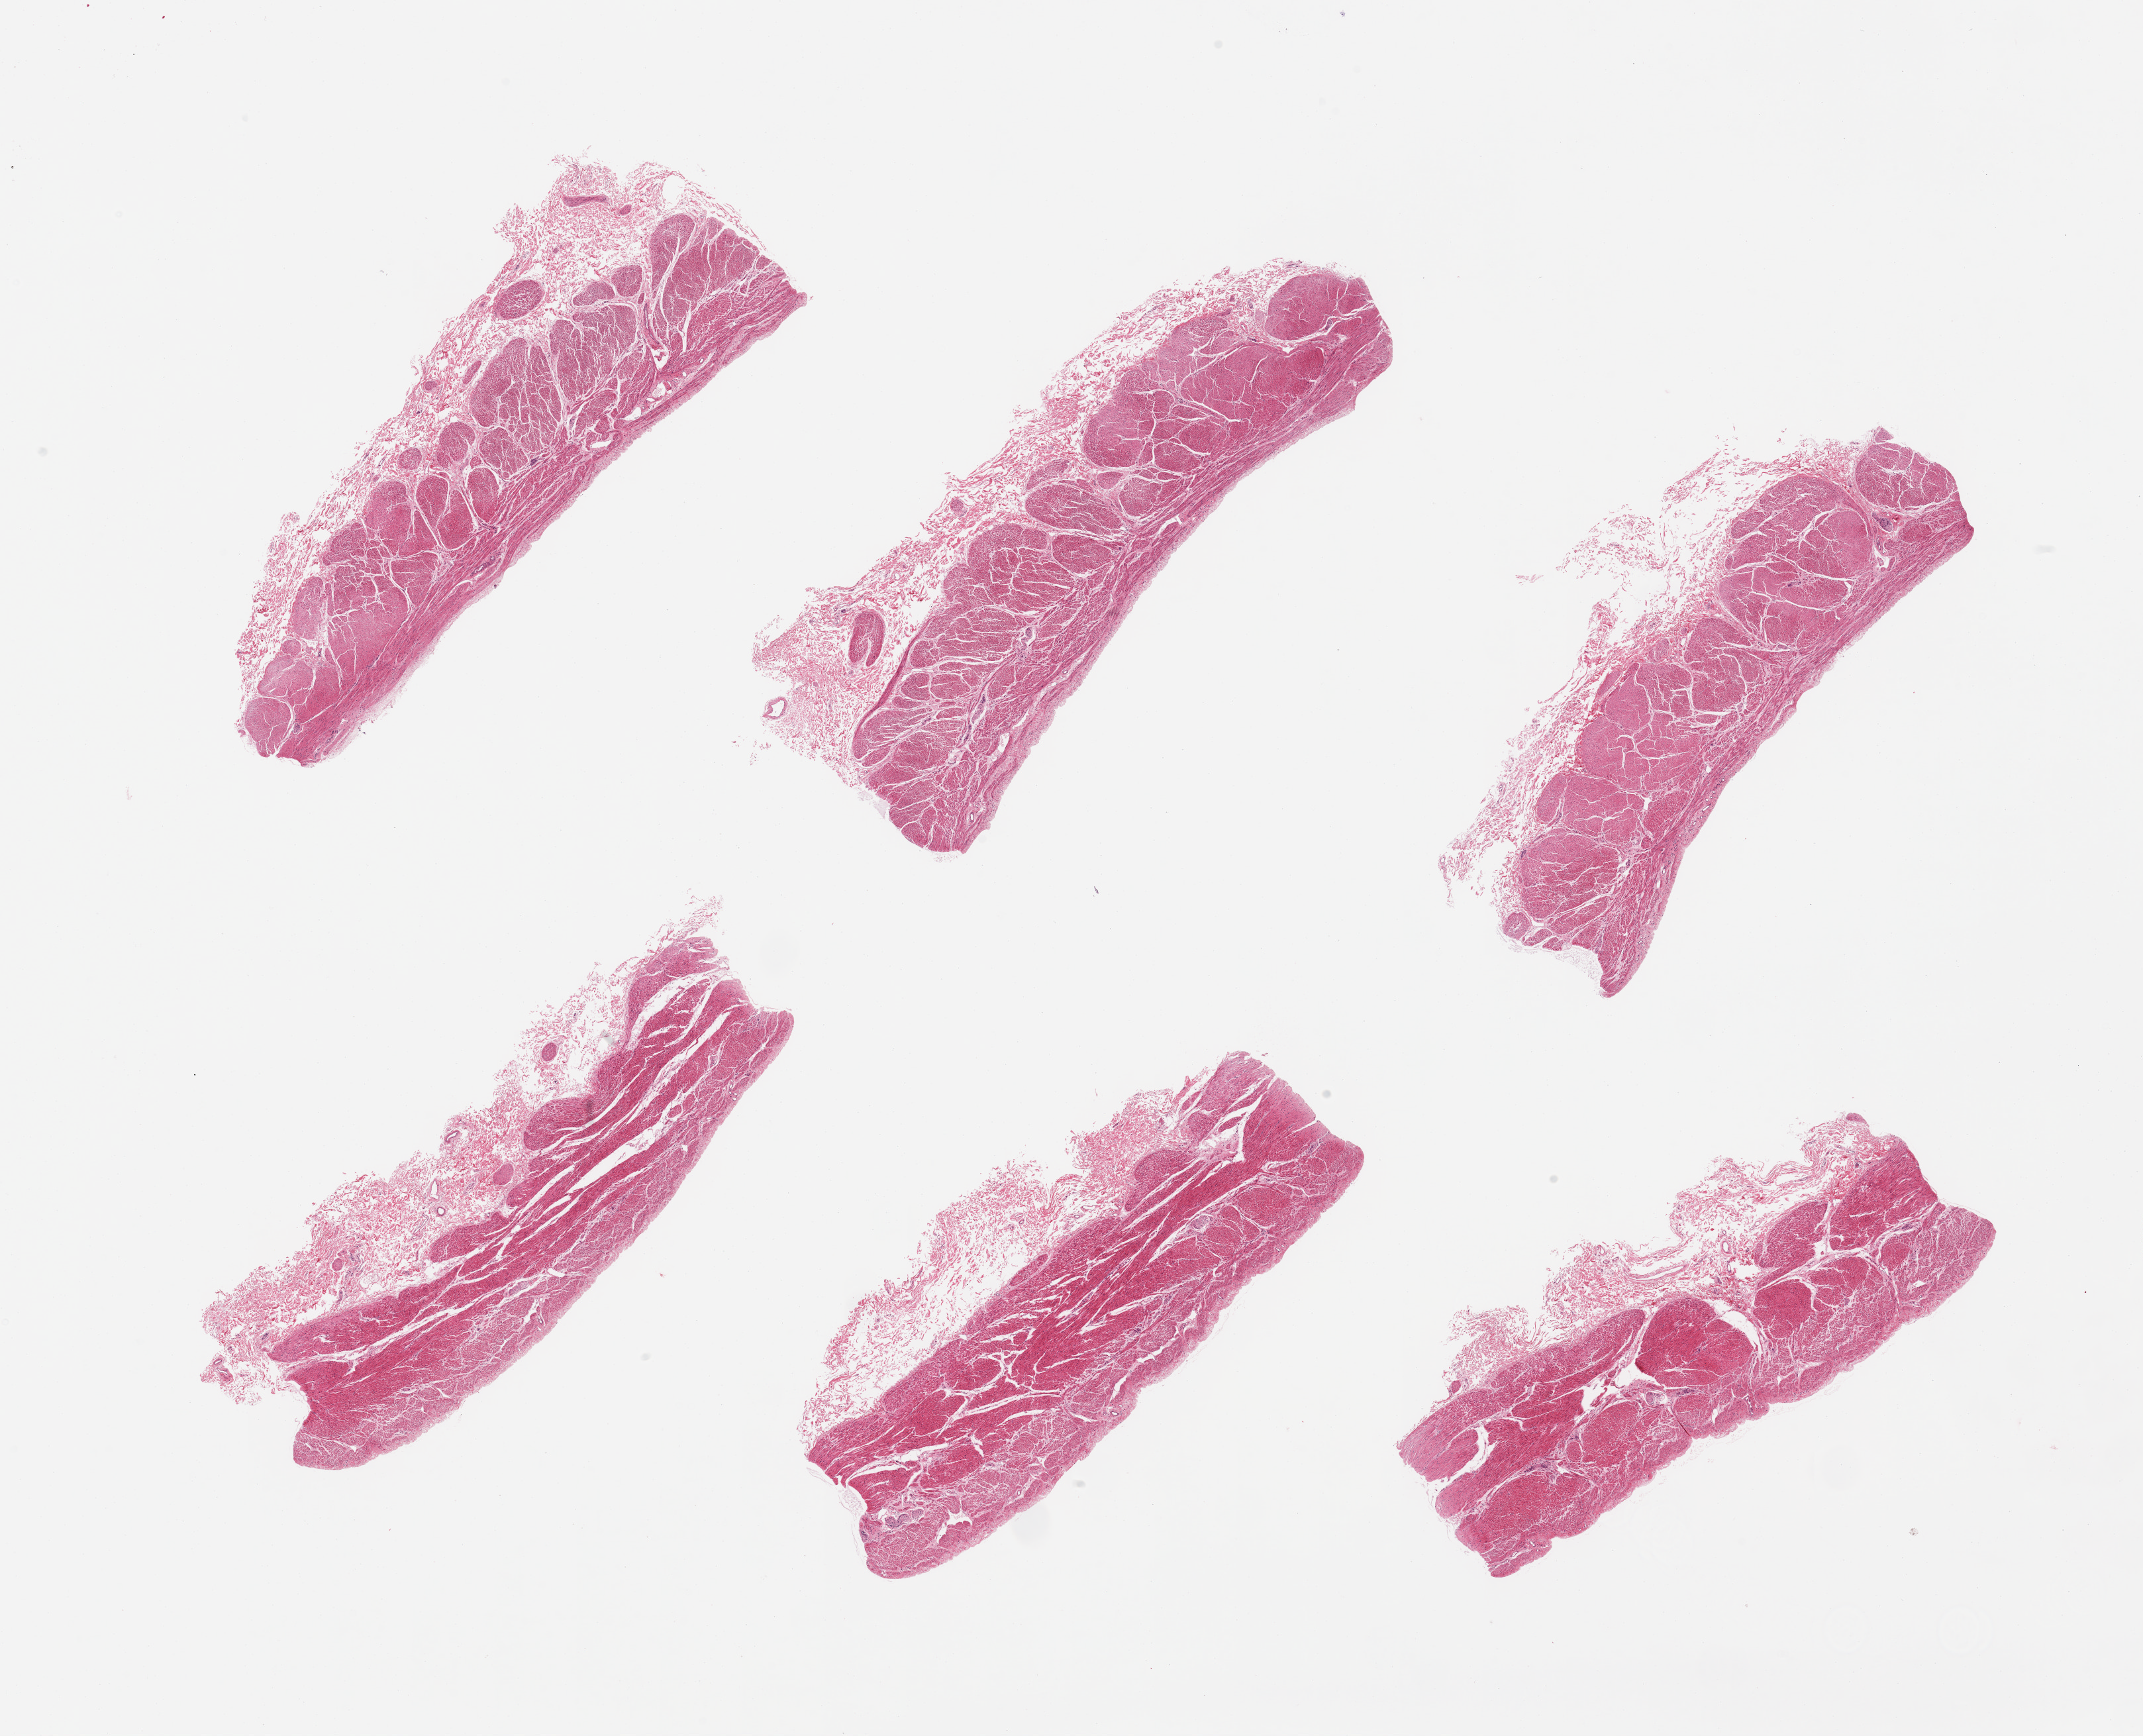
H&E whole-slide image, whole scanned area (about 25.6 x 20.7 mm) shown as a low-resolution overview. PAXgene-fixed, paraffin-embedded tissue. Sampled site (target tissue): stomach. Donor tissue sample. Male donor.
Pathologist's review note for this sample: 6 pieces, mucosa completely sloughed.